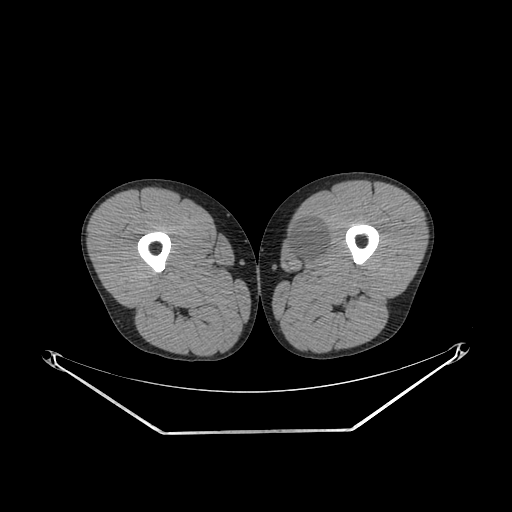
CT of an extremity soft-tissue mass (from a PET/CT study), one axial slice; slice 255 of 311 in the series (ordered by position); 140 kVp; soft-tissue window (W 400 / L 40 HU); 3.75 mm slice thickness; 512 × 512 image matrix, field of view 500 × 500 mm. Male patient. Case-level facts recorded for this patient, not image findings: histological type: mixoid liposarcoma; grade: low; site of the primary tumour: left thigh.
Structures marked on this image (expert contour drawn on MRI and transferred to this co-registered scan by the dataset authors):
- gross tumour volume (mass): bounding box (x1, y1, x2, y2) in pixels: (286, 219, 330, 264)